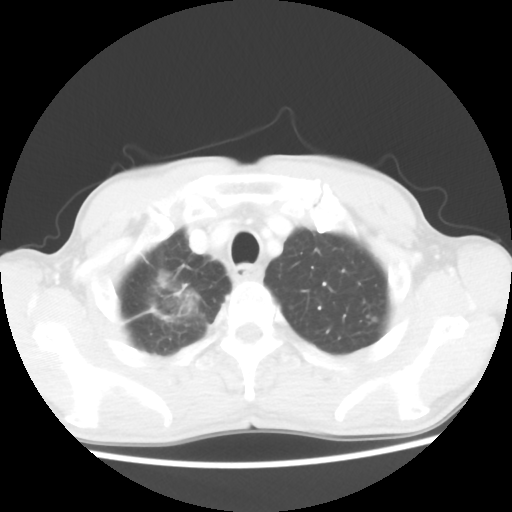
Chest CT, one axial slice; position 46 of 52 along the scan axis; 100 kVp; lung window (W 1500 / L -600 HU); 5 mm slice thickness; 512 × 512 image matrix. Patient: male, 66 years. Case-level facts recorded for this patient, not image findings: clinical TNM (as recorded): T2 N0 M1a.
Outlined on this slice (bounding box drawn by a radiologist):
- lung tumour (recorded histology: adenocarcinoma): bounding box <148,267,205,328> (left, top, right, bottom; pixels)